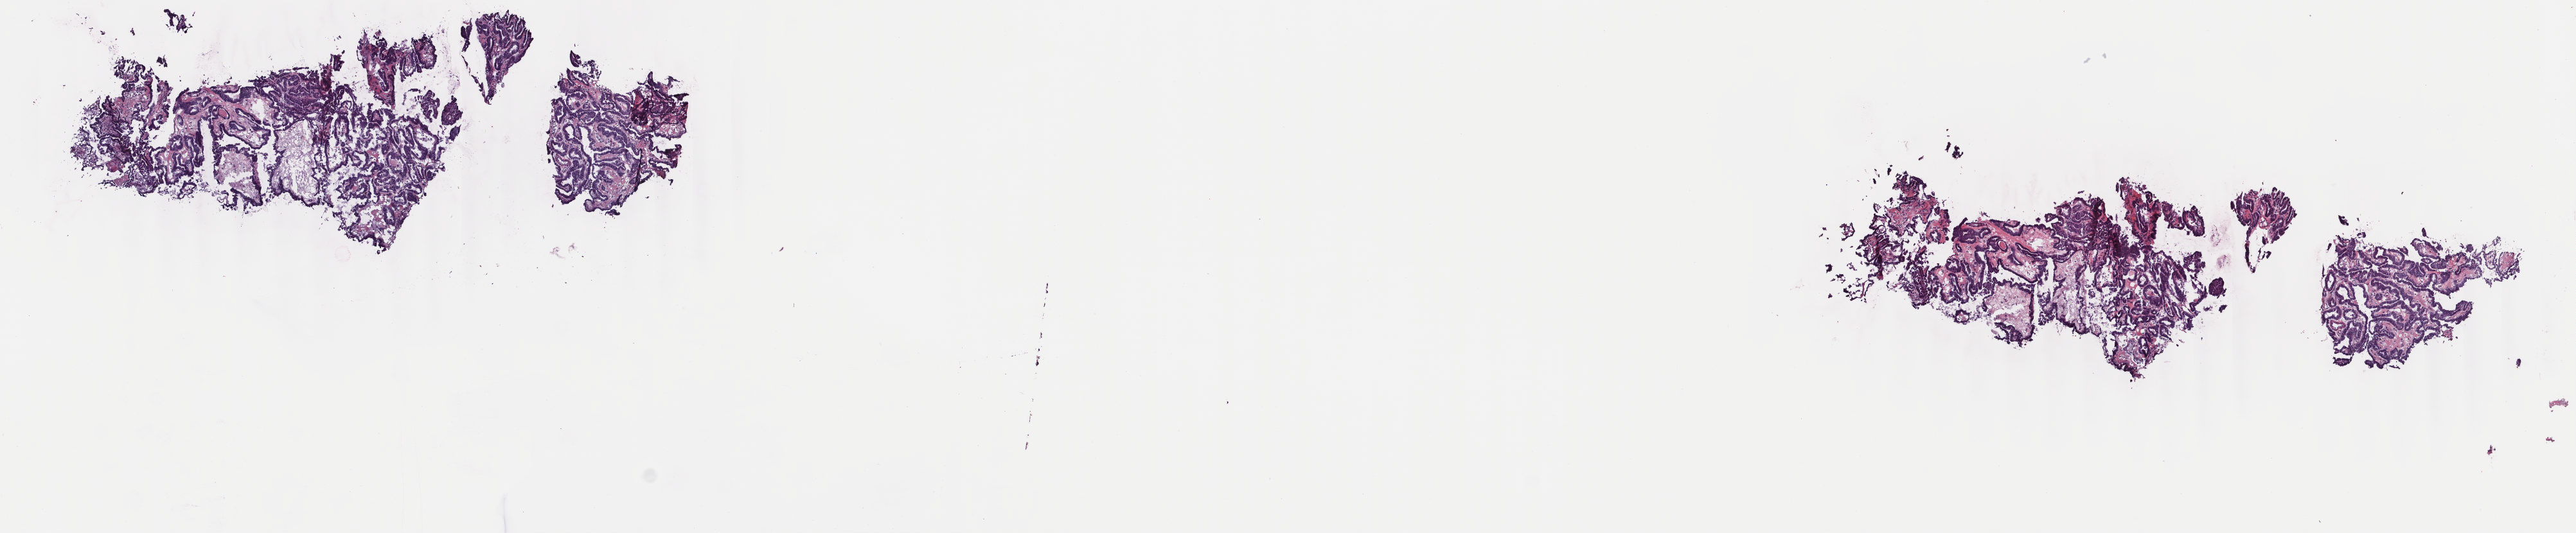
Whole-slide histology image, H&E — shown as a low-resolution overview of the whole scanned area (about 15.9 x 3.3 mm, acquisition: 40x scan). Frozen section. Thyroid, primary tumour sample. Male, age 35 years at initial diagnosis. Pathologist review of this section (percent, as recorded): tumour cells 100%, tumour nuclei 80%, normal cells 0%, stromal cells 0%, necrosis 0%. Inflammatory infiltration, as recorded: lymphocyte infiltration 2%, monocyte infiltration 1%, neutrophil infiltration 0%.
• lymph nodes positive (case pathology): 40 of 77 examined
• AJCC pathologic stage: I (7th edition)
• laterality: right
• histologic diagnosis: Papillary adenocarcinoma, NOS (thyroid gland)